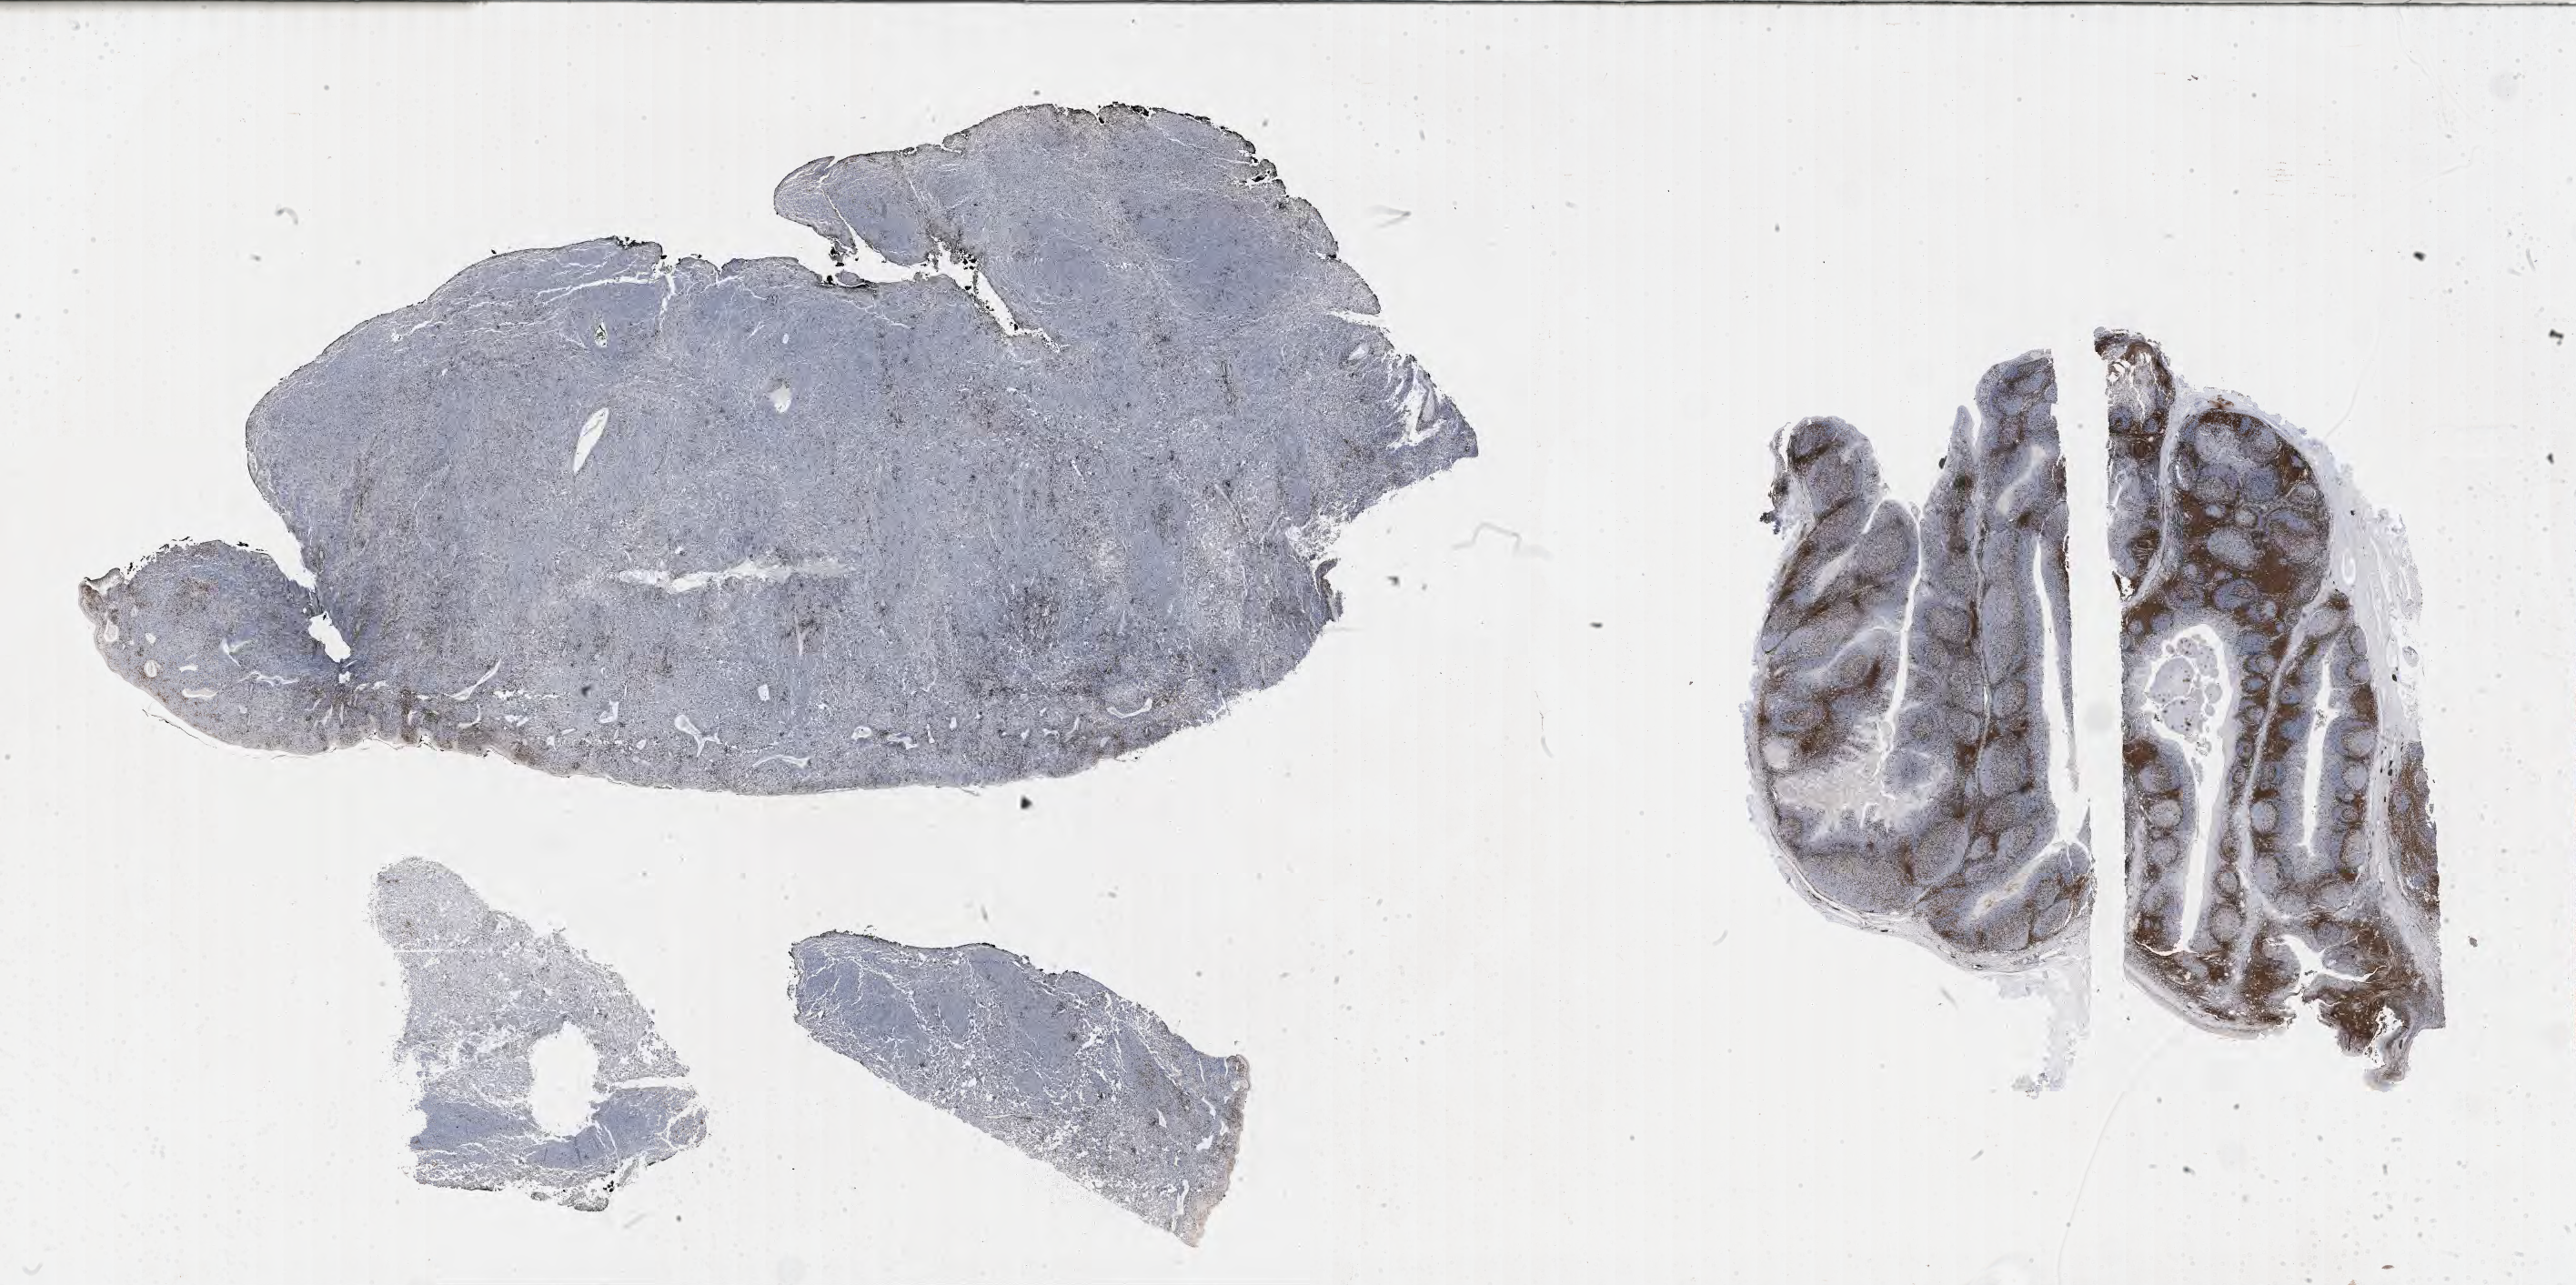
IHC for CD3, whole-slide image — whole scanned area (about 45.8 x 22.8 mm) shown as a low-resolution overview, specimen: tumor tissue. Male patient, aged 46.
Diagnosis: Burkitt lymphoma, NOS.